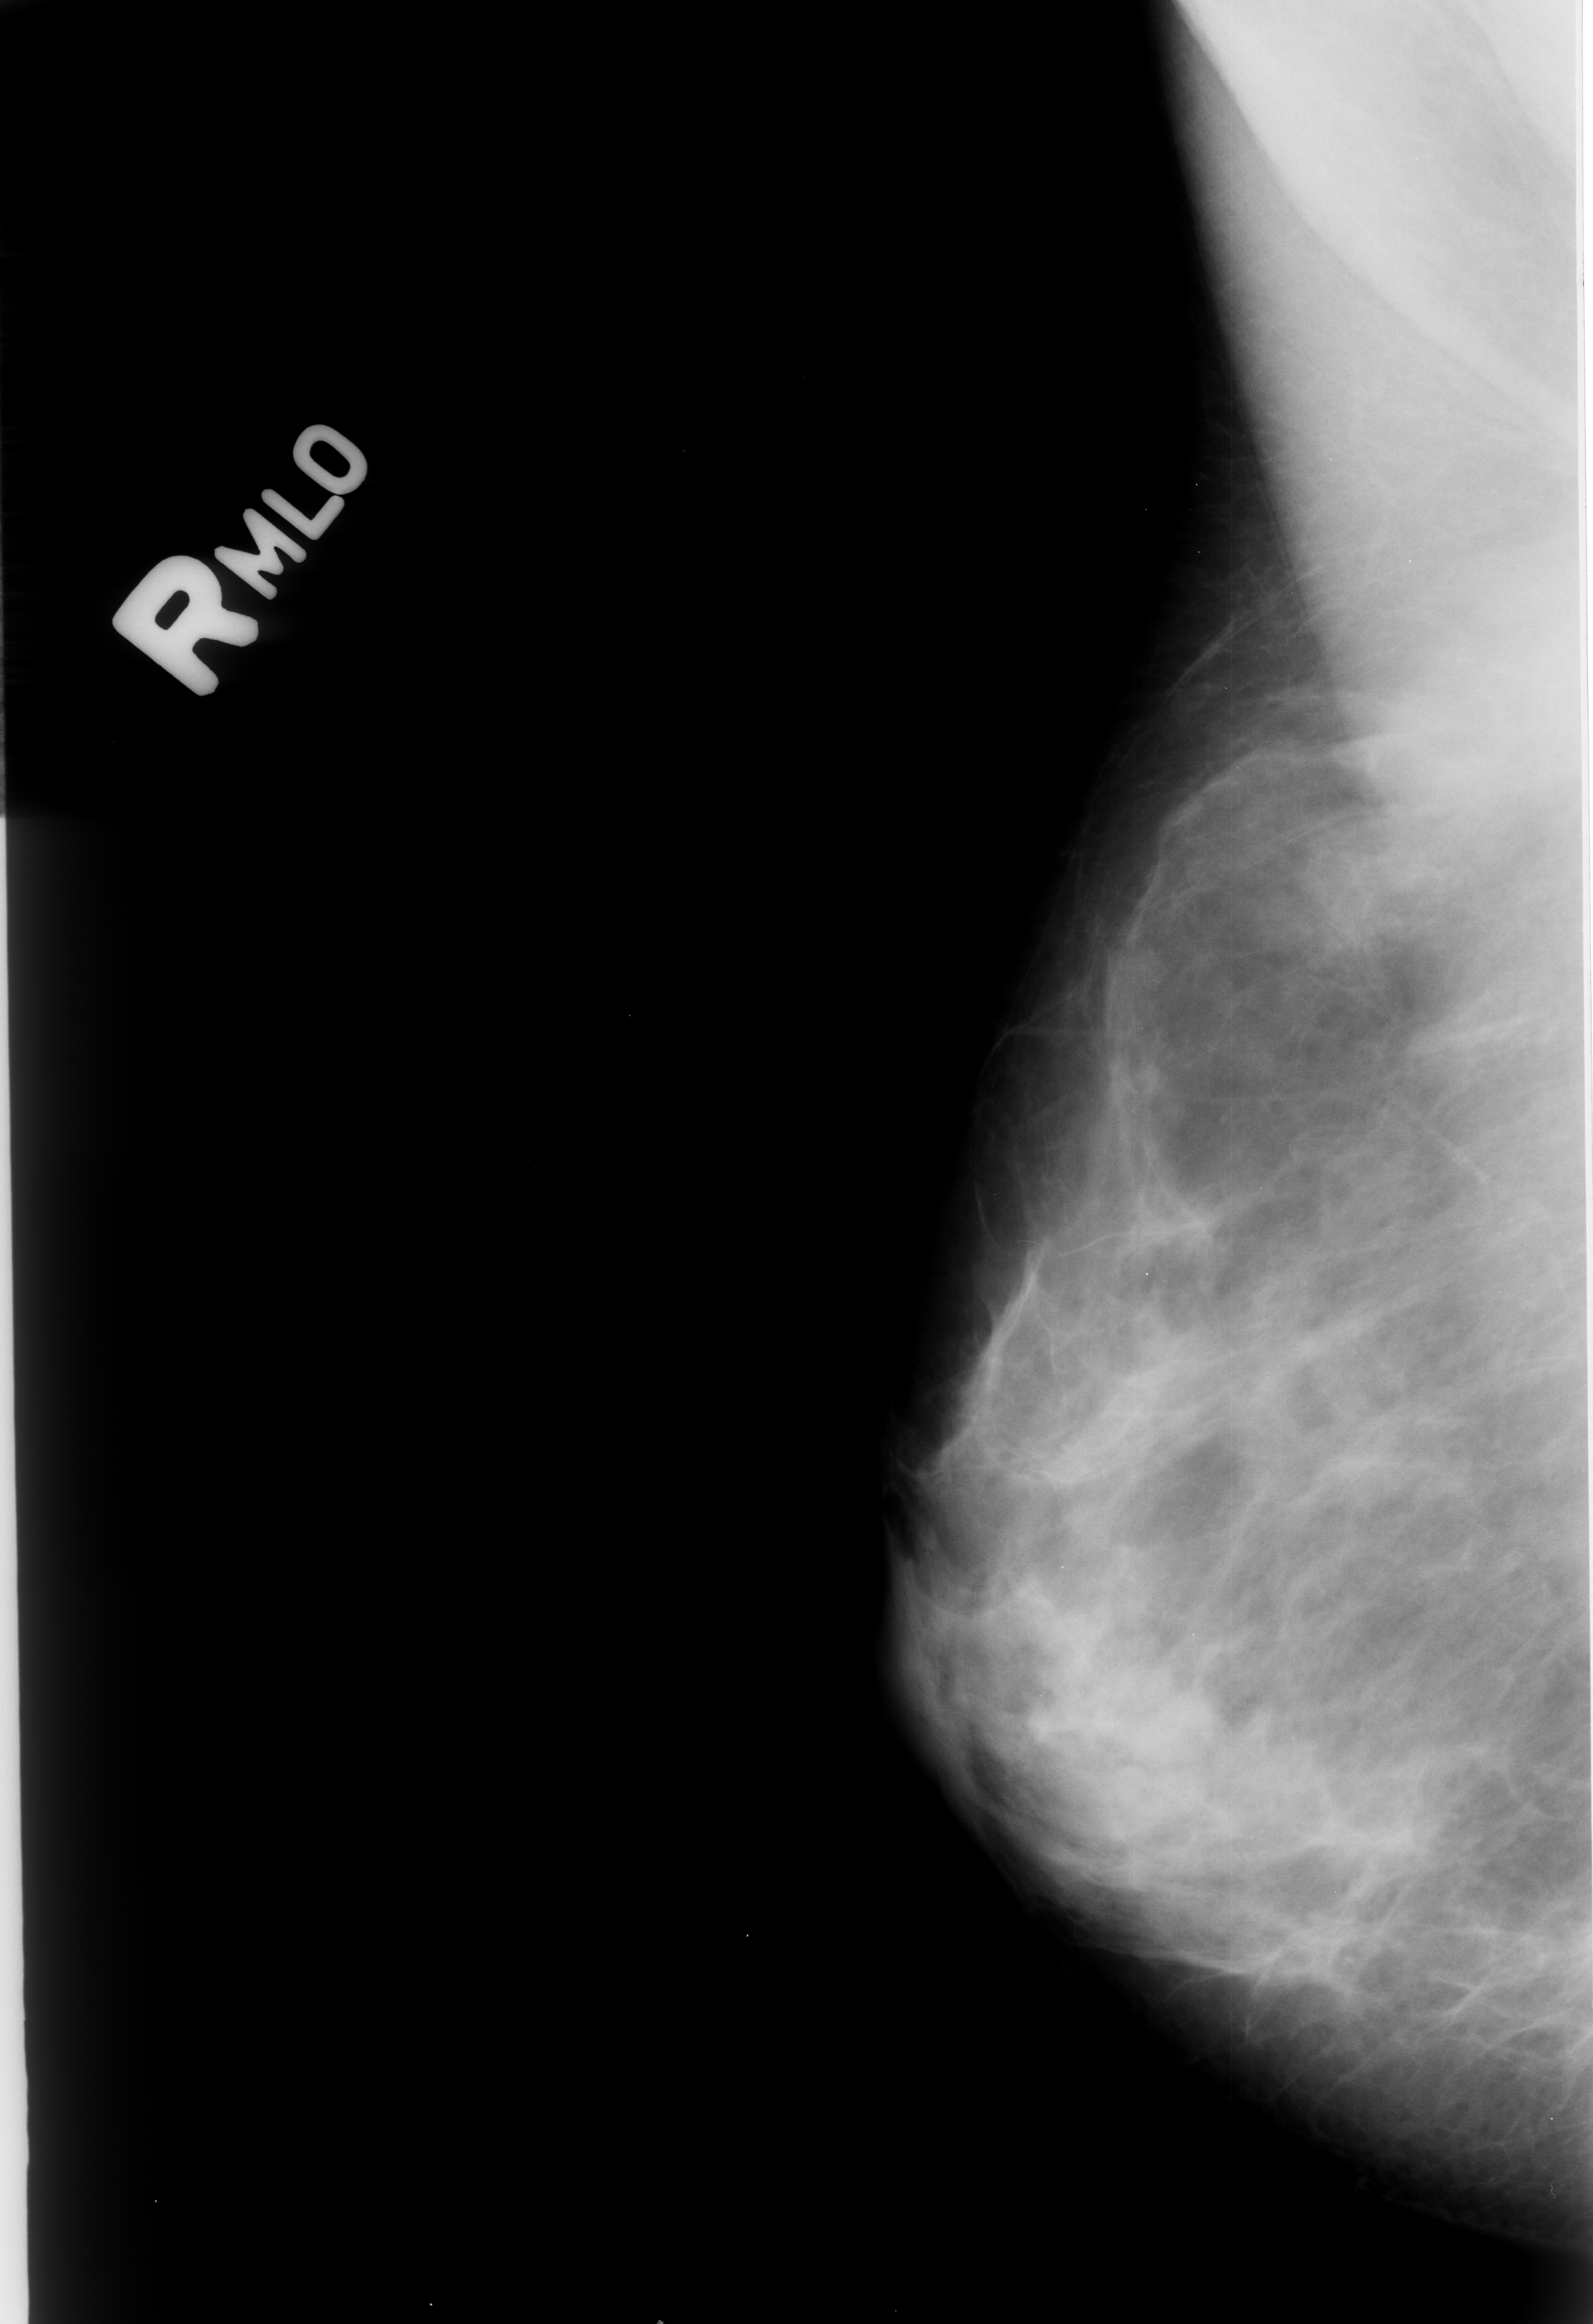
Digitized screen-film mammogram; right breast; mediolateral oblique (MLO) view; BI-RADS breast density category 3 (scale 1–4); 1593 × 2324 image matrix.
Marked abnormalities (boxes around the expert regions of interest):
- mass, shape focal asymmetric density; BI-RADS assessment category 2; outcome (as recorded, no biopsy): benign without callback (not worked up further): bounding box <1334,527,1593,842> (left, top, right, bottom; pixels)